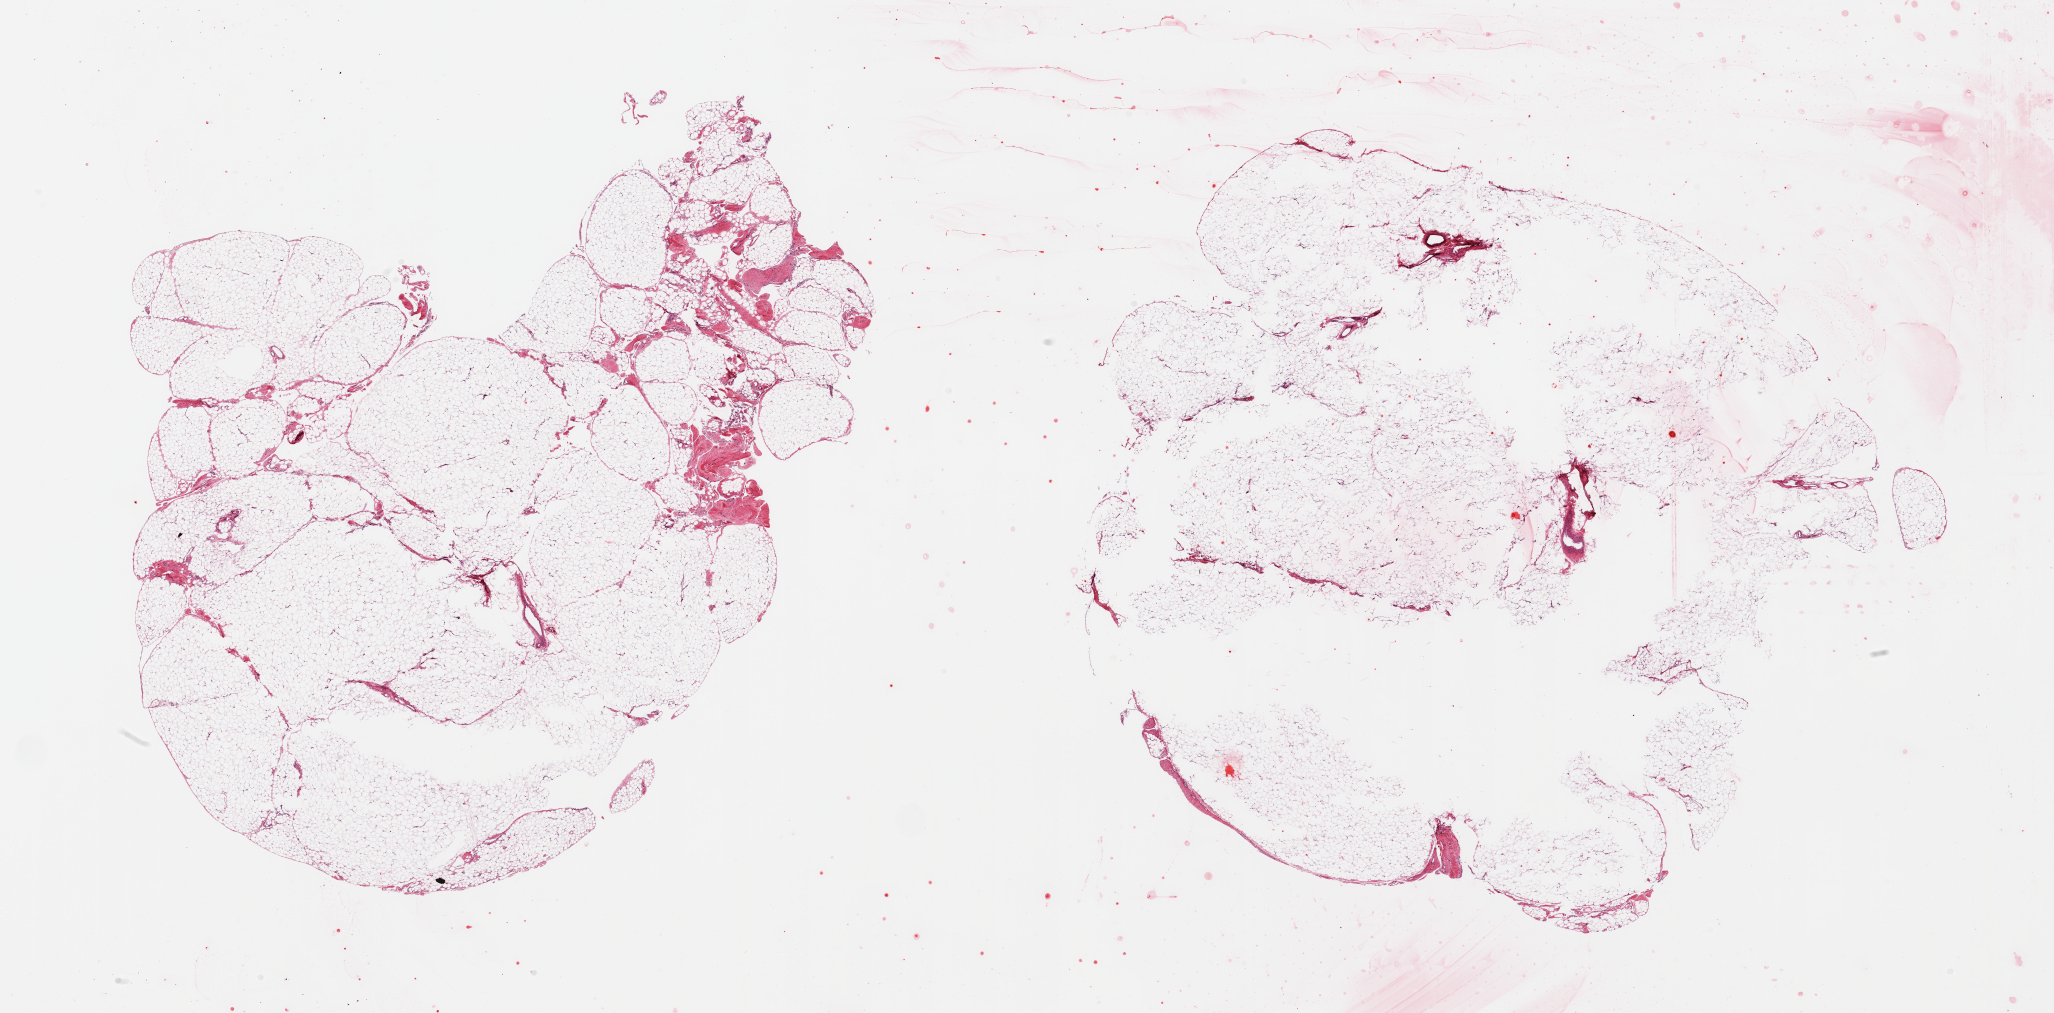
Whole-slide image, hematoxylin and eosin (H&E) stain — a low-resolution overview of the entire scanned area, about 32.5 x 16.0 mm. PAXgene-fixed, paraffin-embedded tissue. Sampled site (target tissue): omentum. Tissue donor sample. Donor sex: female.
Review note (as recorded): 2 pieces; lobulated mature fat, central defects (?poor fixation).